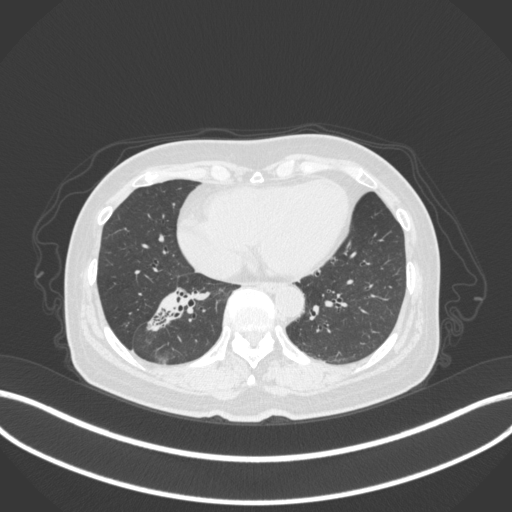
Chest CT, one axial slice. Position 139 of 429 along the scan axis. Reconstruction kernel B31f. 120 kVp. Lung window (W 1500 / L -600 HU). 1 mm slice thickness. 512 × 512 image matrix, field of view 400 × 400 mm. Patient: female, 67 years. From the clinical record (not read from this slice): clinical TNM (as recorded): T1c N1 M0; histopathological grade: G2-3.
Outlined on this slice (bounding box drawn by a radiologist):
- lung tumour (recorded histology: adenocarcinoma): bounding box [x1, y1, x2, y2] px = [148, 282, 216, 334]